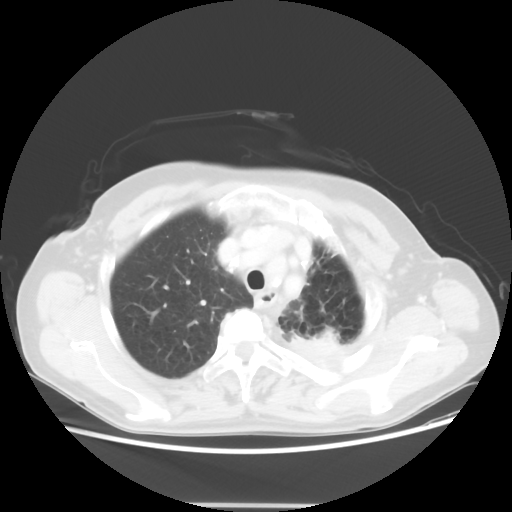
Chest CT, one axial slice; position 43 of 56 along the scan axis; 100 kVp; lung window (W 1500 / L -600 HU); 512 × 512 image matrix, field of view 377 × 377 mm. Female patient, age 63 years. Case-level facts recorded for this patient, not image findings: clinical TNM (as recorded): T2a N0 M0.
Outlined on this slice (rectangle marked by the reading radiologist):
- lung tumour (recorded histology: adenocarcinoma): bounding box <291,327,349,362> (left, top, right, bottom; pixels)